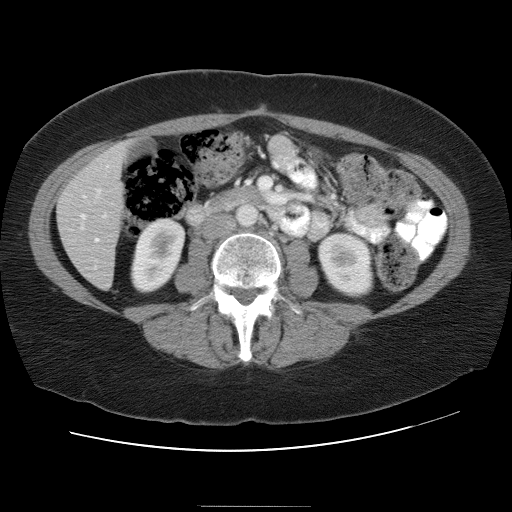
Contrast-enhanced abdominal CT, one axial slice; position 9 of 30 along the scan axis; reconstruction kernel STANDARD; intravenous contrast given; soft-tissue window (W 400 / L 40 HU); 7.5 mm slice thickness; 512 × 512 image matrix, field of view 376 × 376 mm. Female patient, age 52 years. From the clinical record (not read from this slice): diagnosis: colorectal cancer liver metastases, imaged before liver resection; multiple liver metastases: no; largest metastasis: 3 cm.
Structures marked on this image (outlined manually by an expert reader):
- hepatic veins: bounding box [x1, y1, x2, y2] px = [81, 215, 85, 219]
- liver: [58, 145, 126, 288]
- portal vein (with intrahepatic branches): [94, 215, 106, 242]